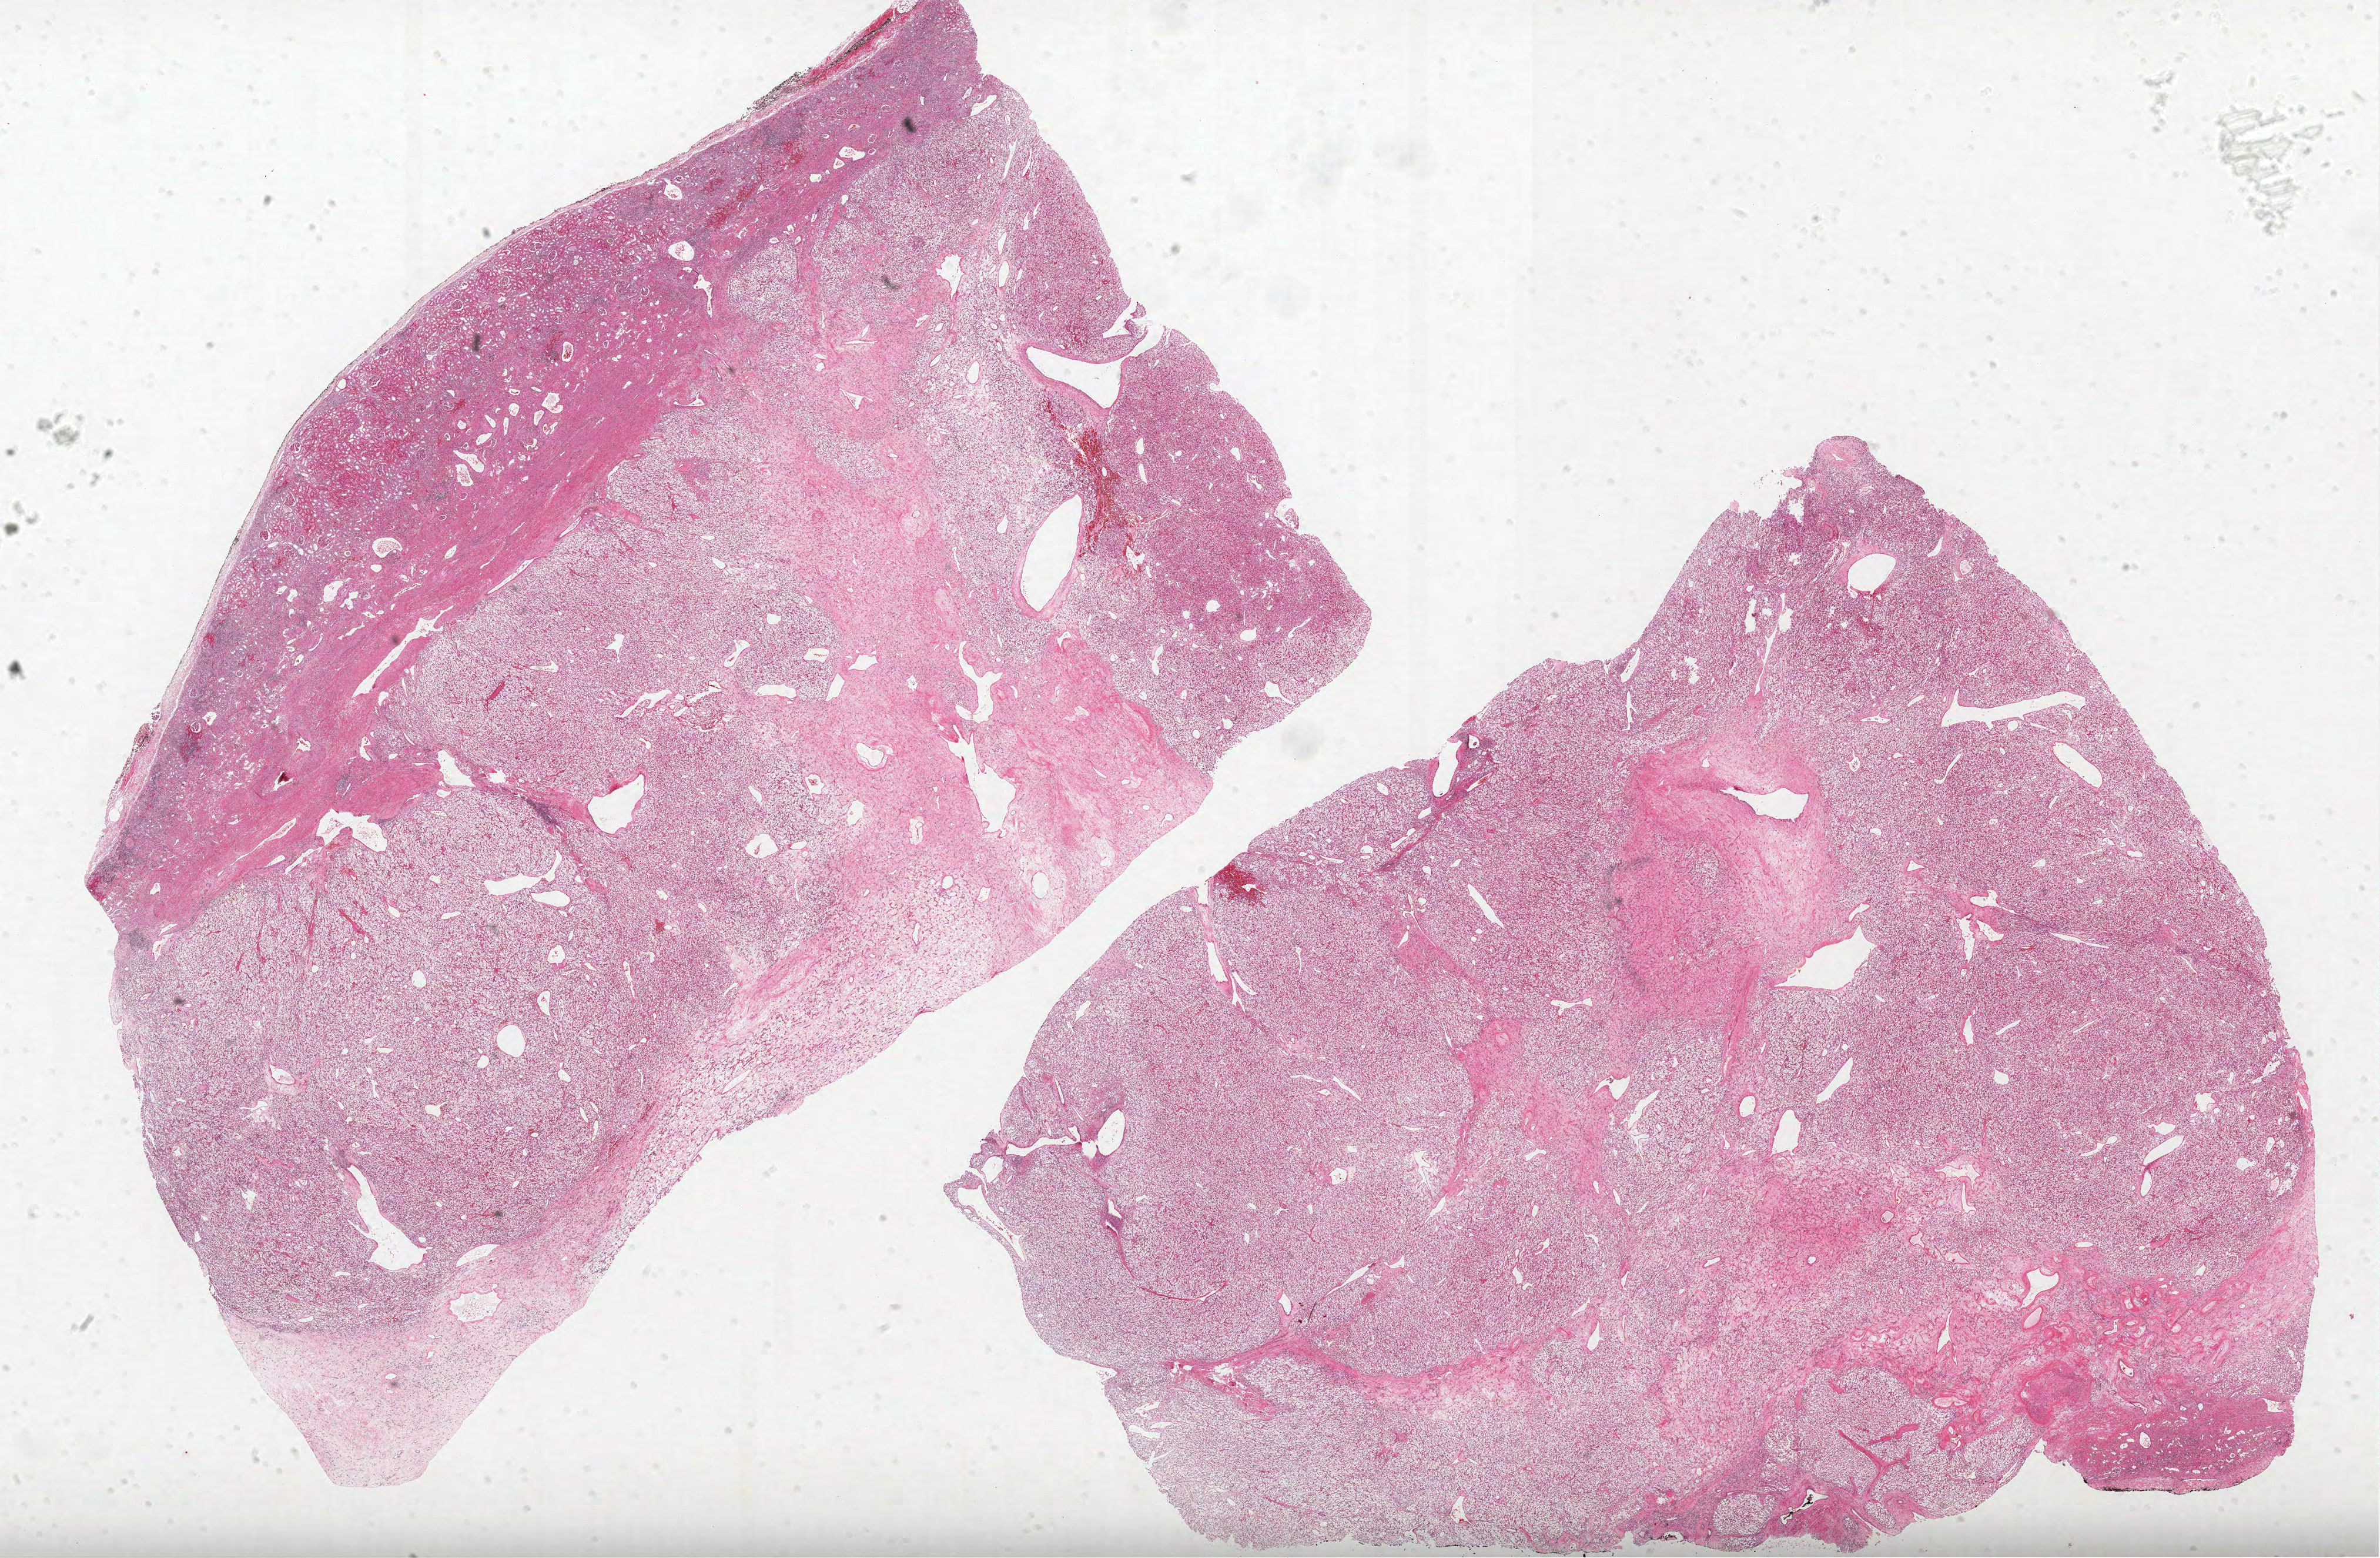
Whole-slide histology image, Hematoxylin and eosin (H&E) stained — a low-resolution overview of the entire scanned area, about 32.4 x 21.2 mm. Formalin-fixed paraffin-embedded (FFPE) diagnostic section. Kidney, primary tumour sample. Female patient; age at initial diagnosis 72 years. Histologic grade: G2 (moderately differentiated).
• lymph nodes positive (case pathology): 0 of 13 examined
• laterality: left
• TNM: T1b N0 M0
• AJCC pathologic stage: I
• histologic diagnosis: Clear cell adenocarcinoma, NOS